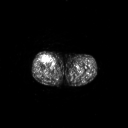
FDG PET of an extremity soft-tissue mass (from a PET/CT study), one axial slice. Position 264 of 311 along the scan axis. 3.27 mm slice thickness. 128 × 128 image matrix, field of view 700 × 700 mm. Male patient, age 56 years. From the clinical record (not read from this slice): histological type: pleiomorphic leiomyosarcoma; grade: intermediate; site of the primary tumour: right thigh.
Structures marked on this image (expert contour drawn on MRI and transferred to this co-registered scan by the dataset authors):
- gross tumour volume including surrounding oedema: box from (x=40, y=55) to (x=51, y=62) px
- gross tumour volume (mass): (x=43, y=56)–(x=50, y=61)